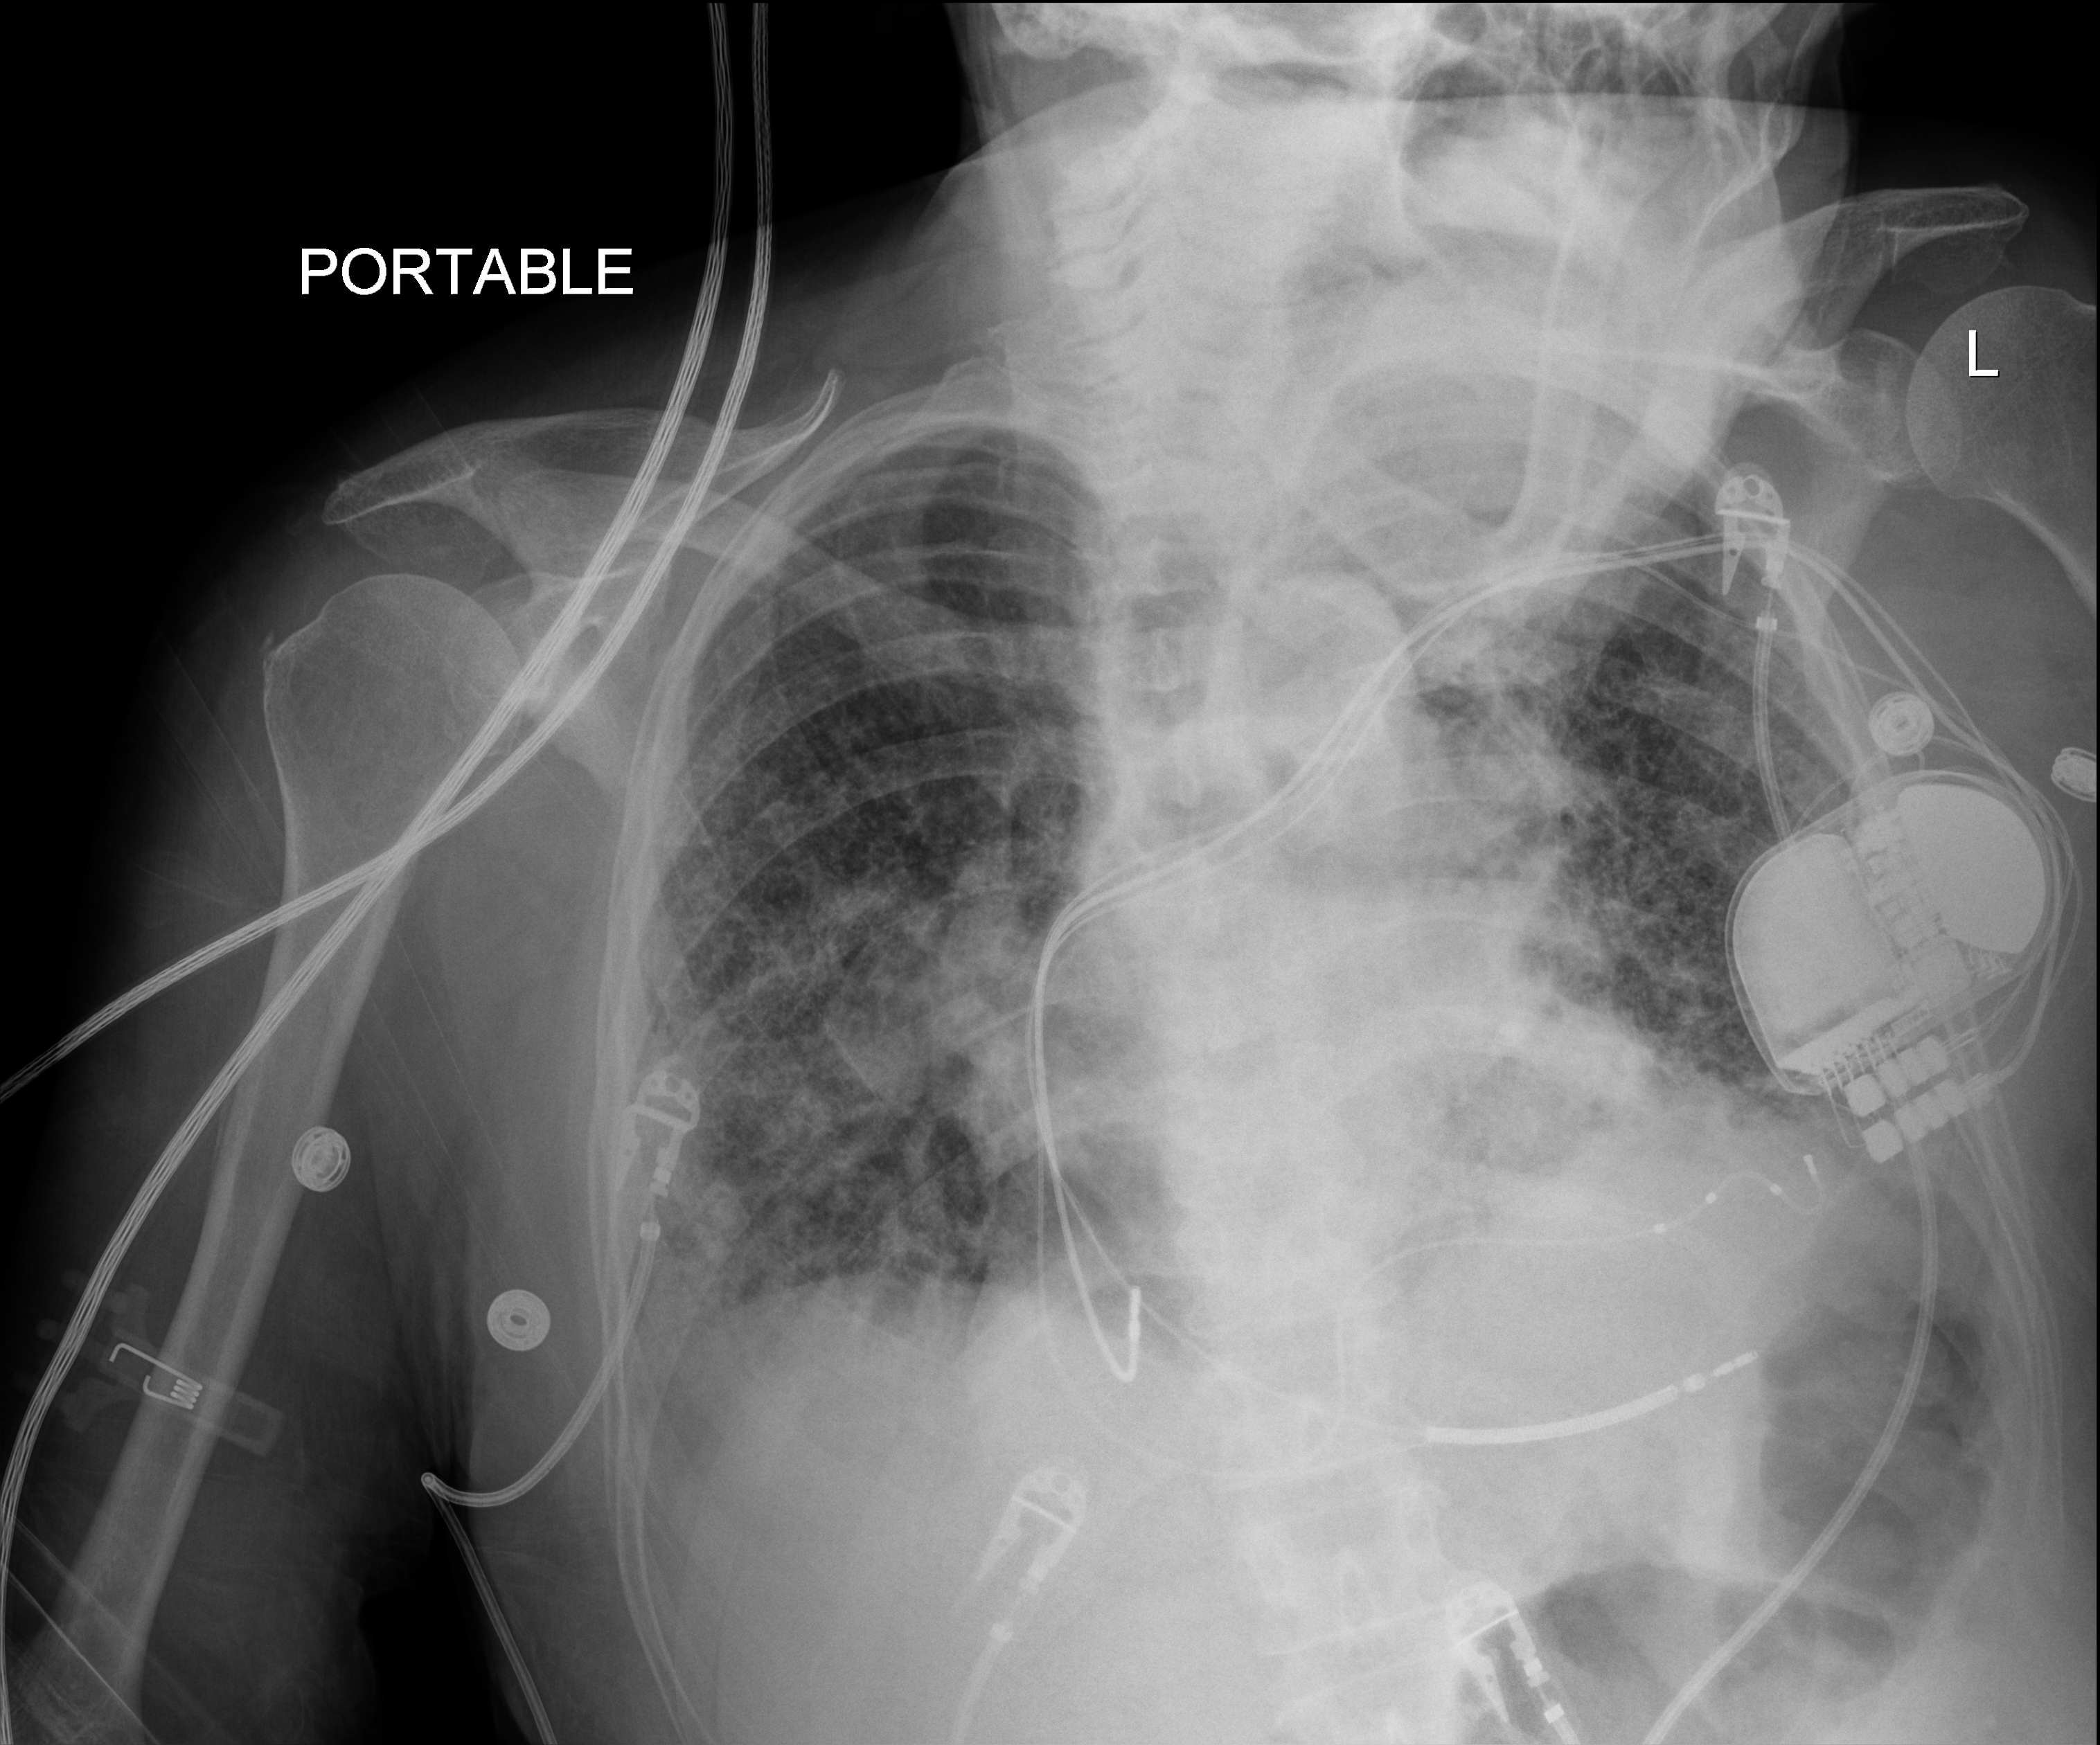
Bedside chest radiograph (digital radiography); anteroposterior (AP) projection. Female patient hospitalised with COVID-19, age 60–74 years.
Hospital-stay facts (about this admission, not read from this image; timing relative to this image not recorded):
- admitted to intensive care during this hospital stay: yes
- length of hospital stay: 6 days